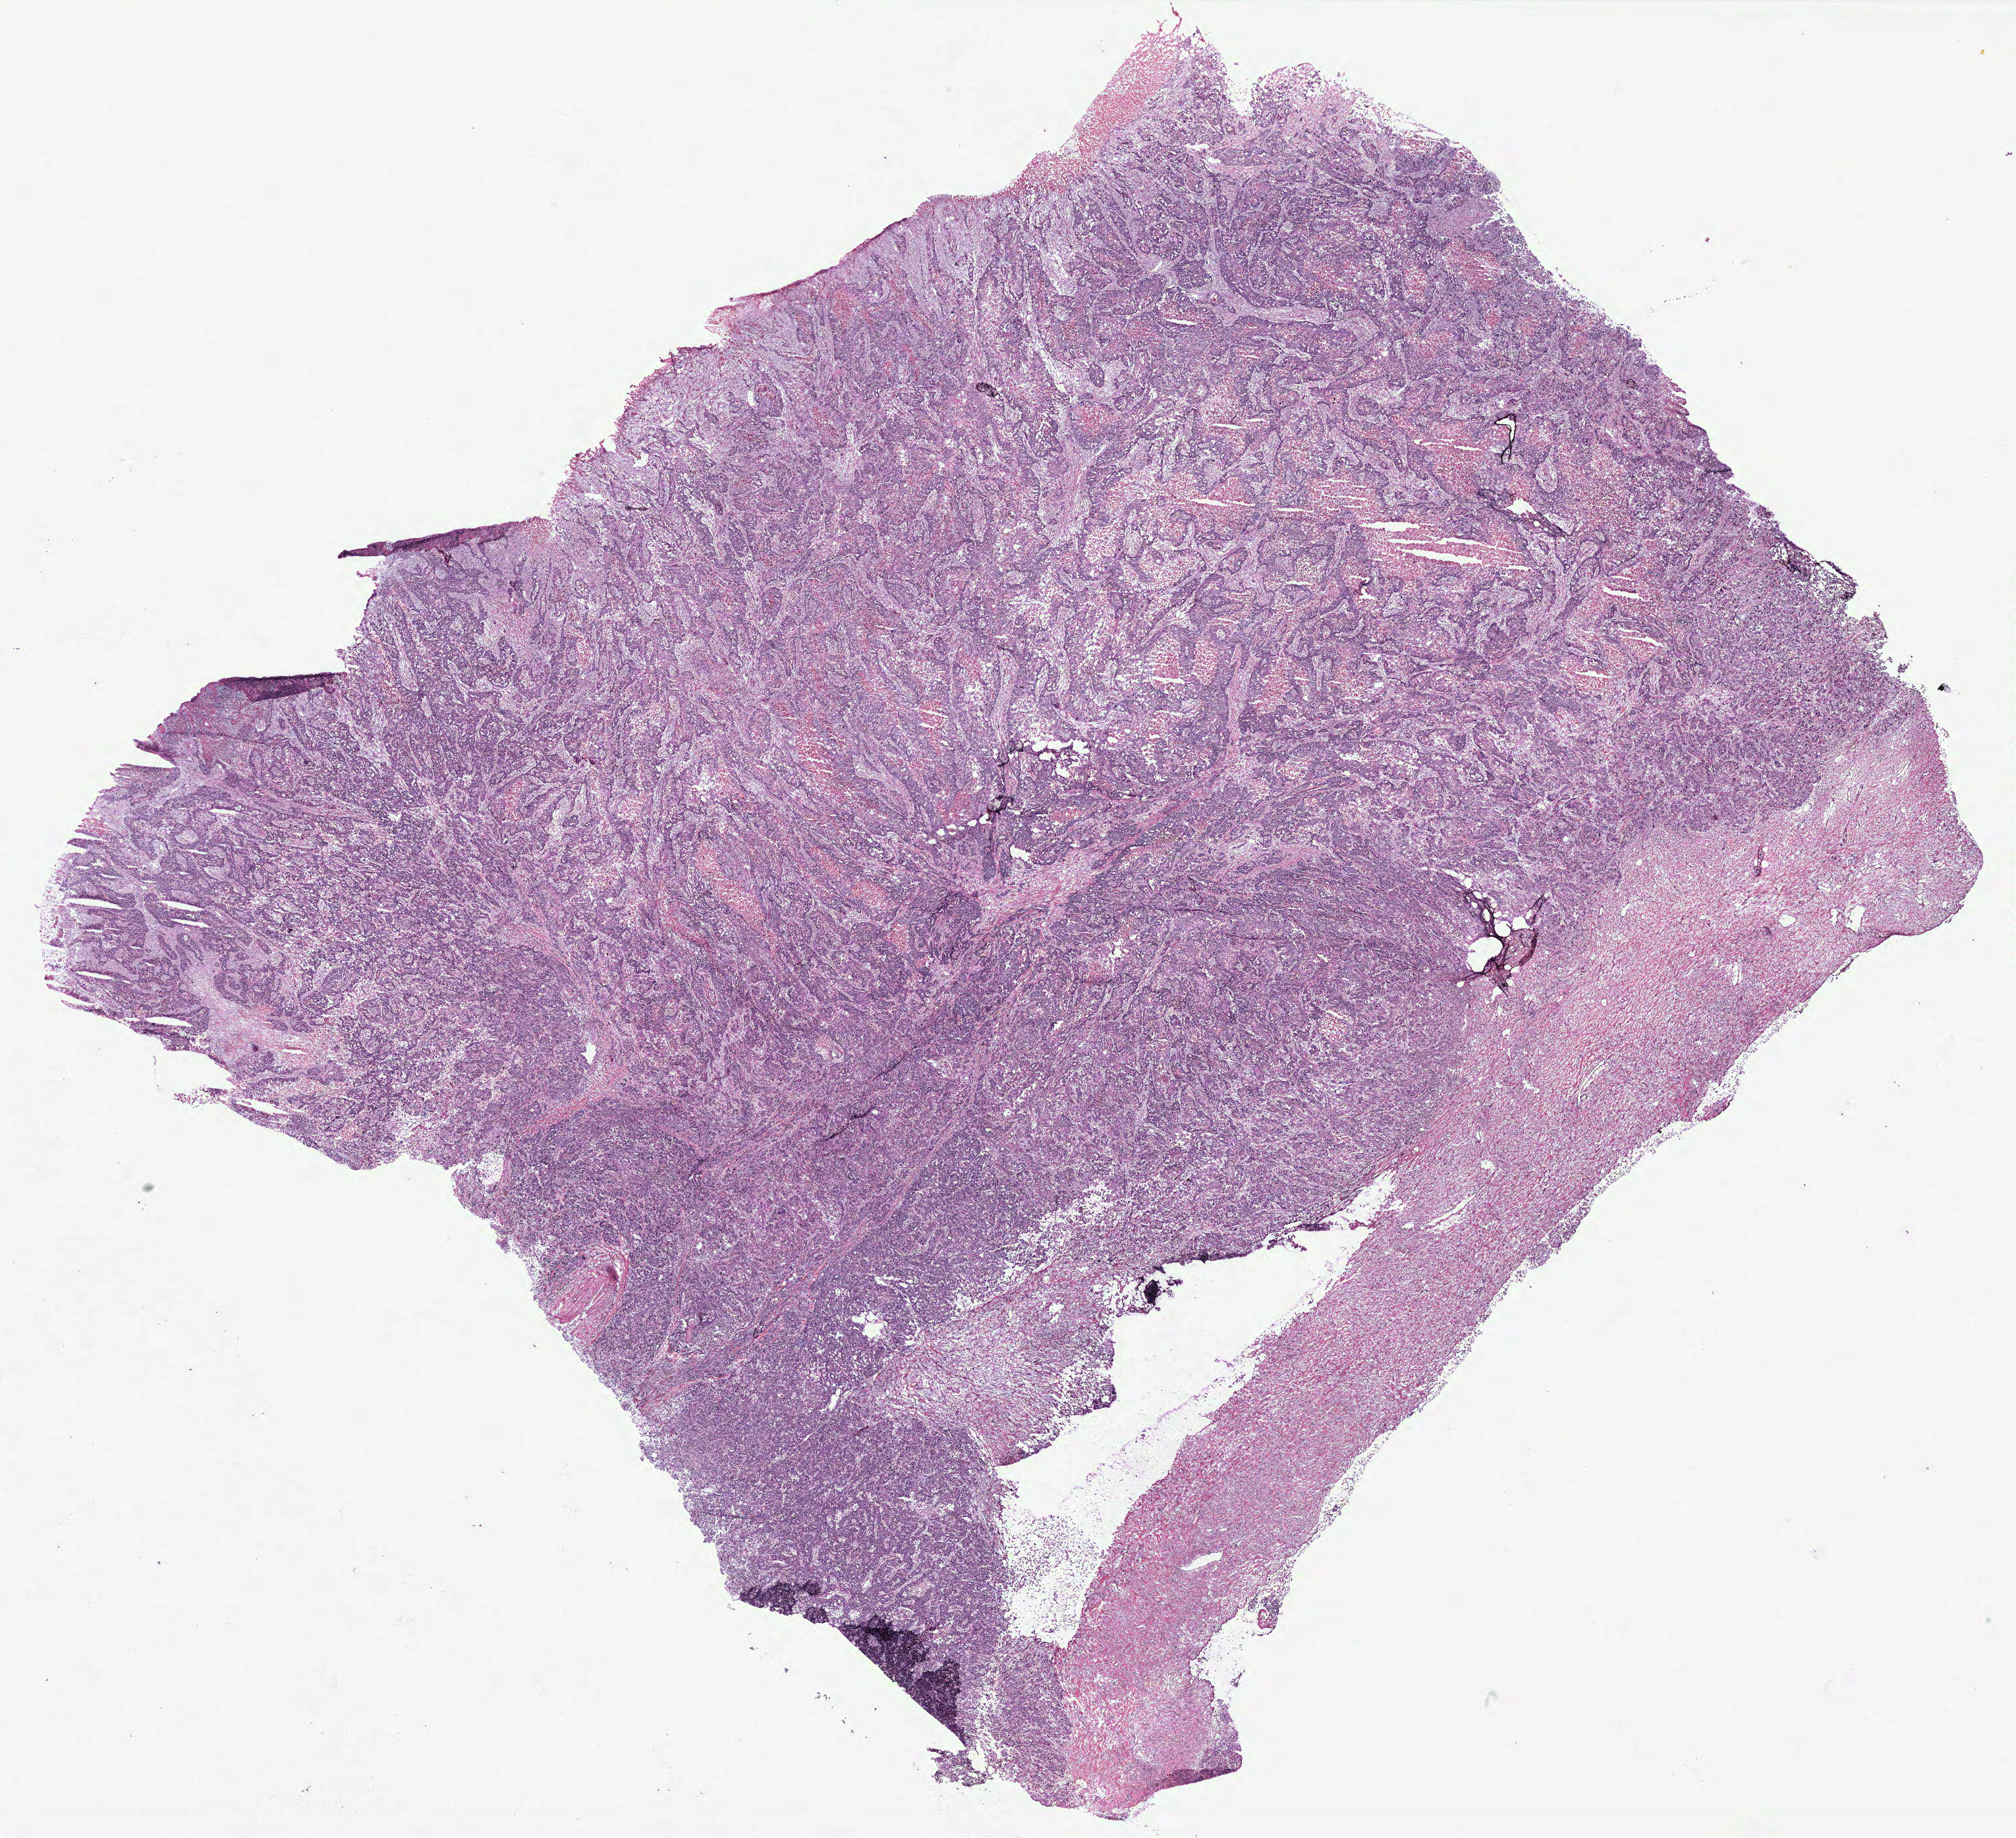
Hematoxylin and eosin (H&E) stained whole-slide image, low-resolution overview of the scanned area, about 24.5 x 22.3 mm (acquisition: 40x scan); colon, tissue type not recorded.
• patient diagnosis (cohort enrolment): colon cancer (colon)